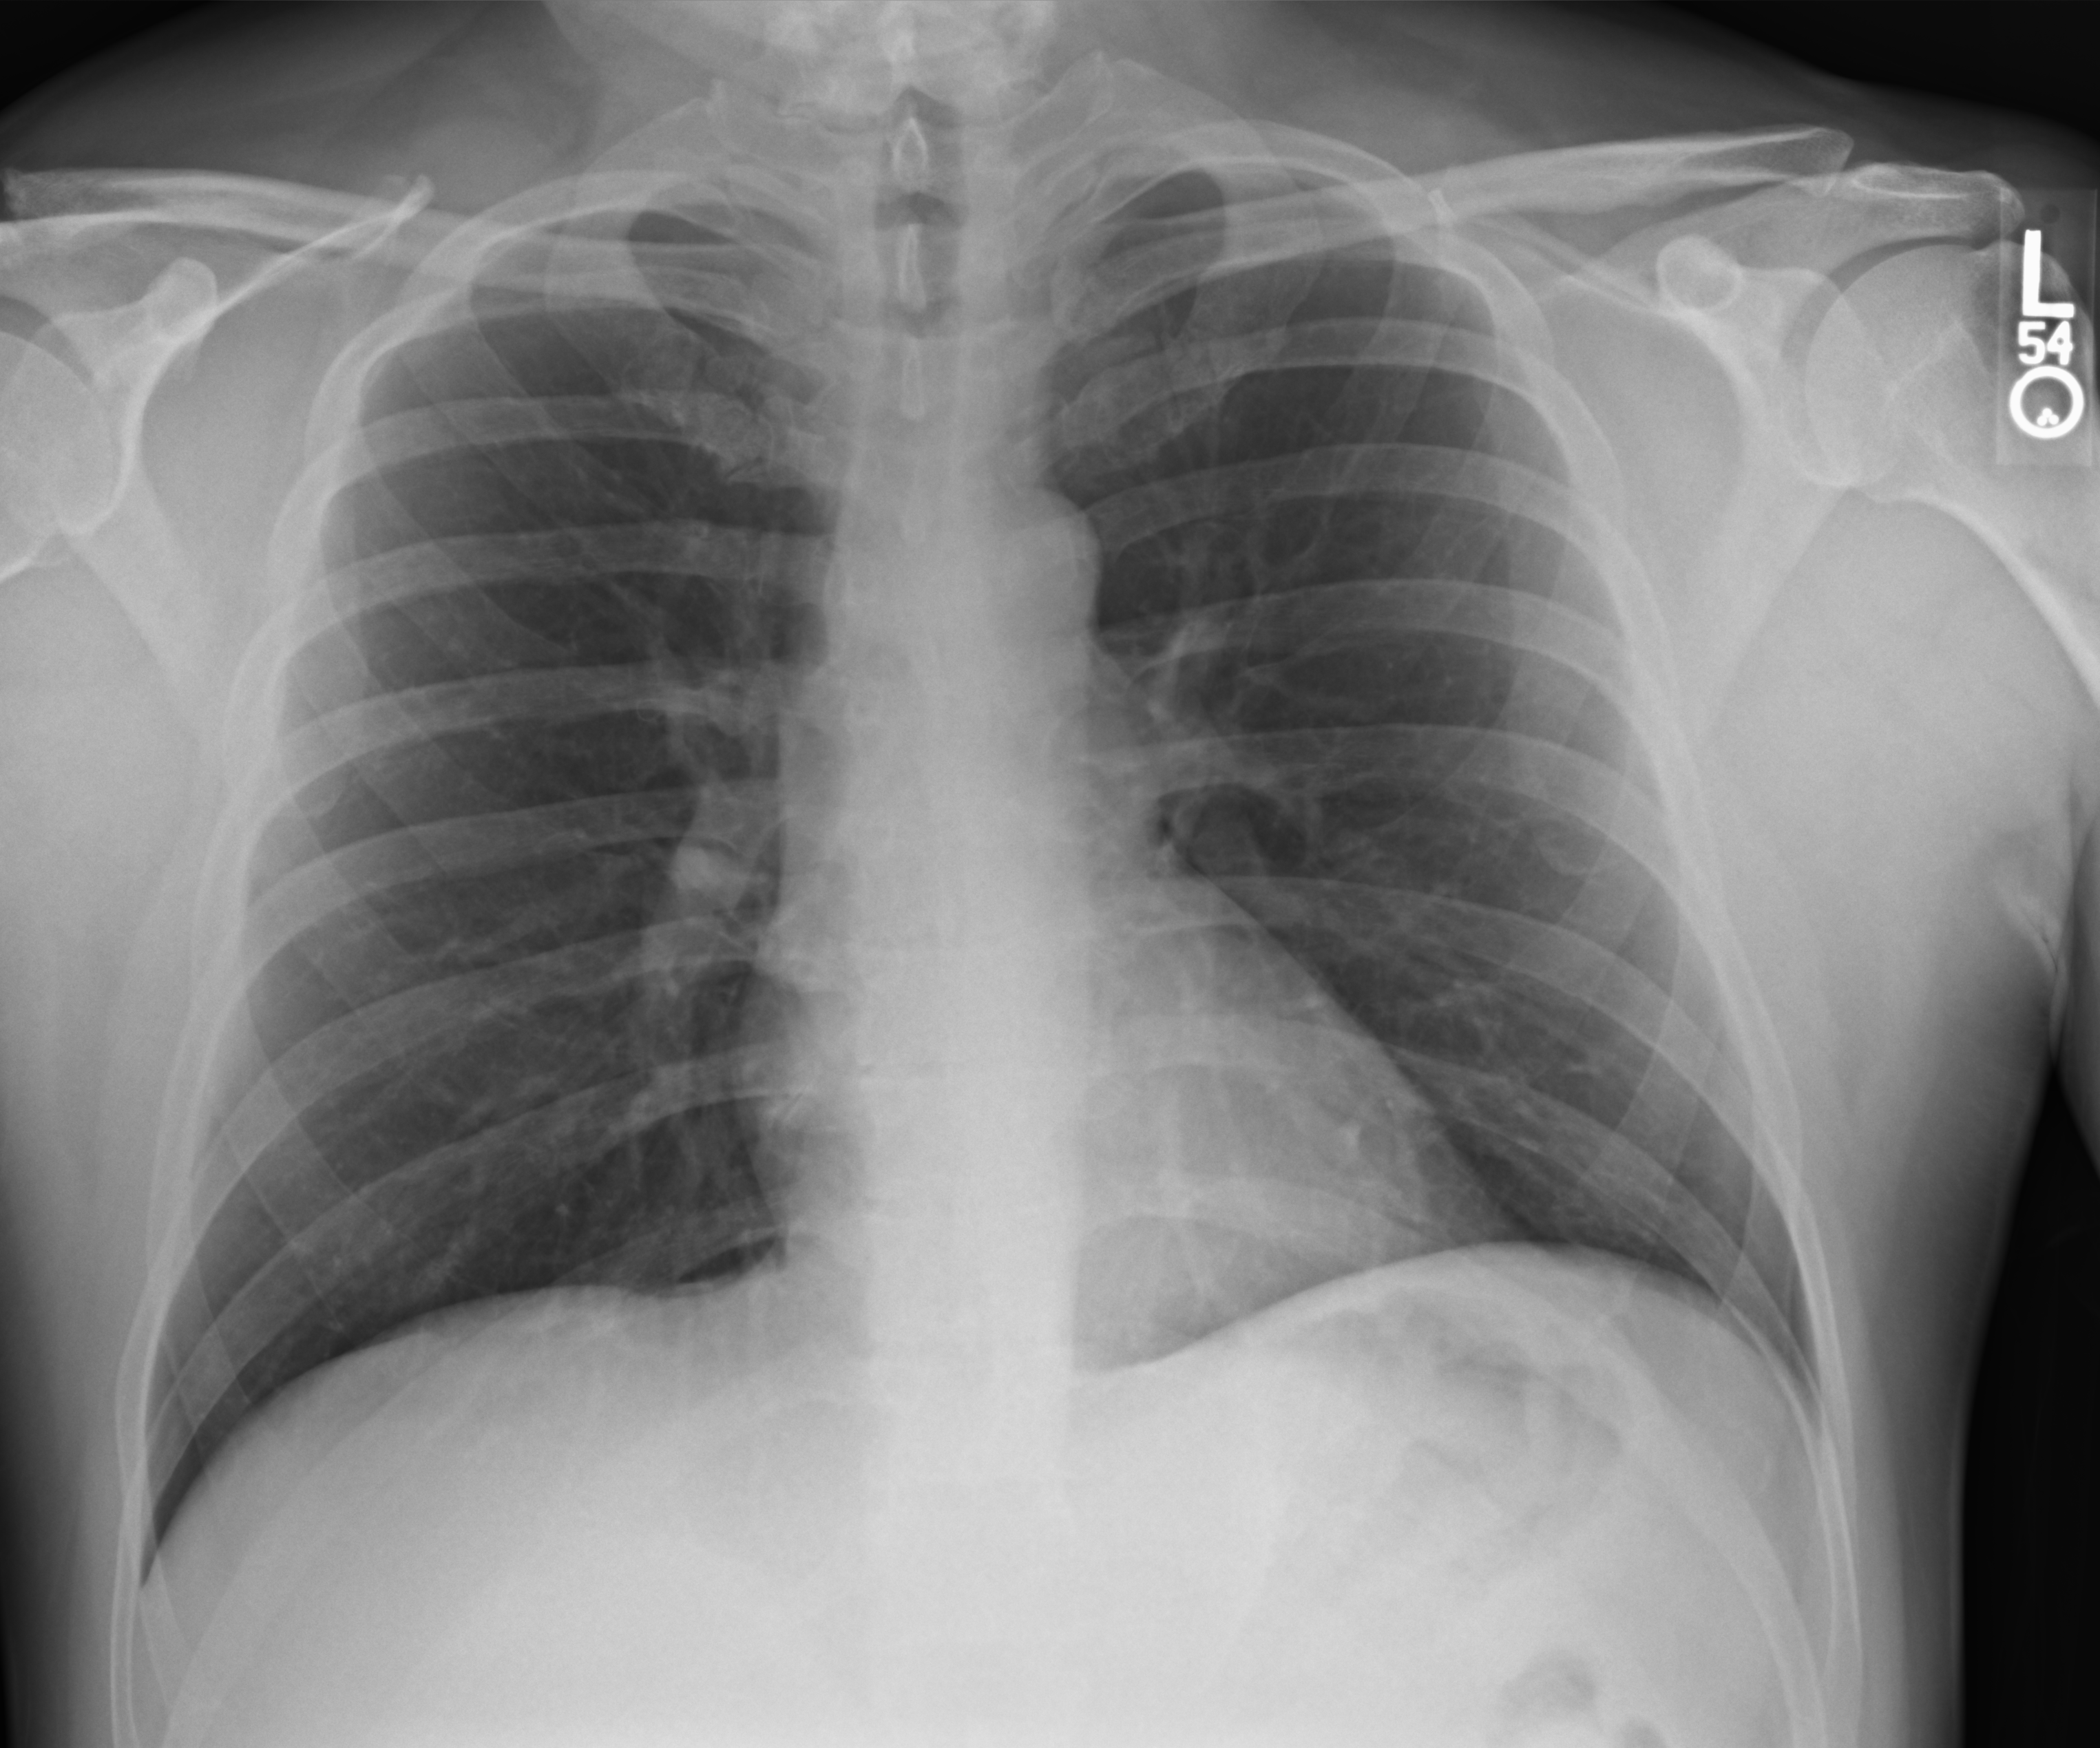
Bedside chest radiograph (computed radiography), anteroposterior (AP) projection. Patient hospitalised with COVID-19; male, aged 18–59 years.
From the hospital-stay record, not from the radiograph (when in the stay this image was taken is not recorded):
- mechanically ventilated during this hospital stay: no
- admitted to intensive care during this hospital stay: no